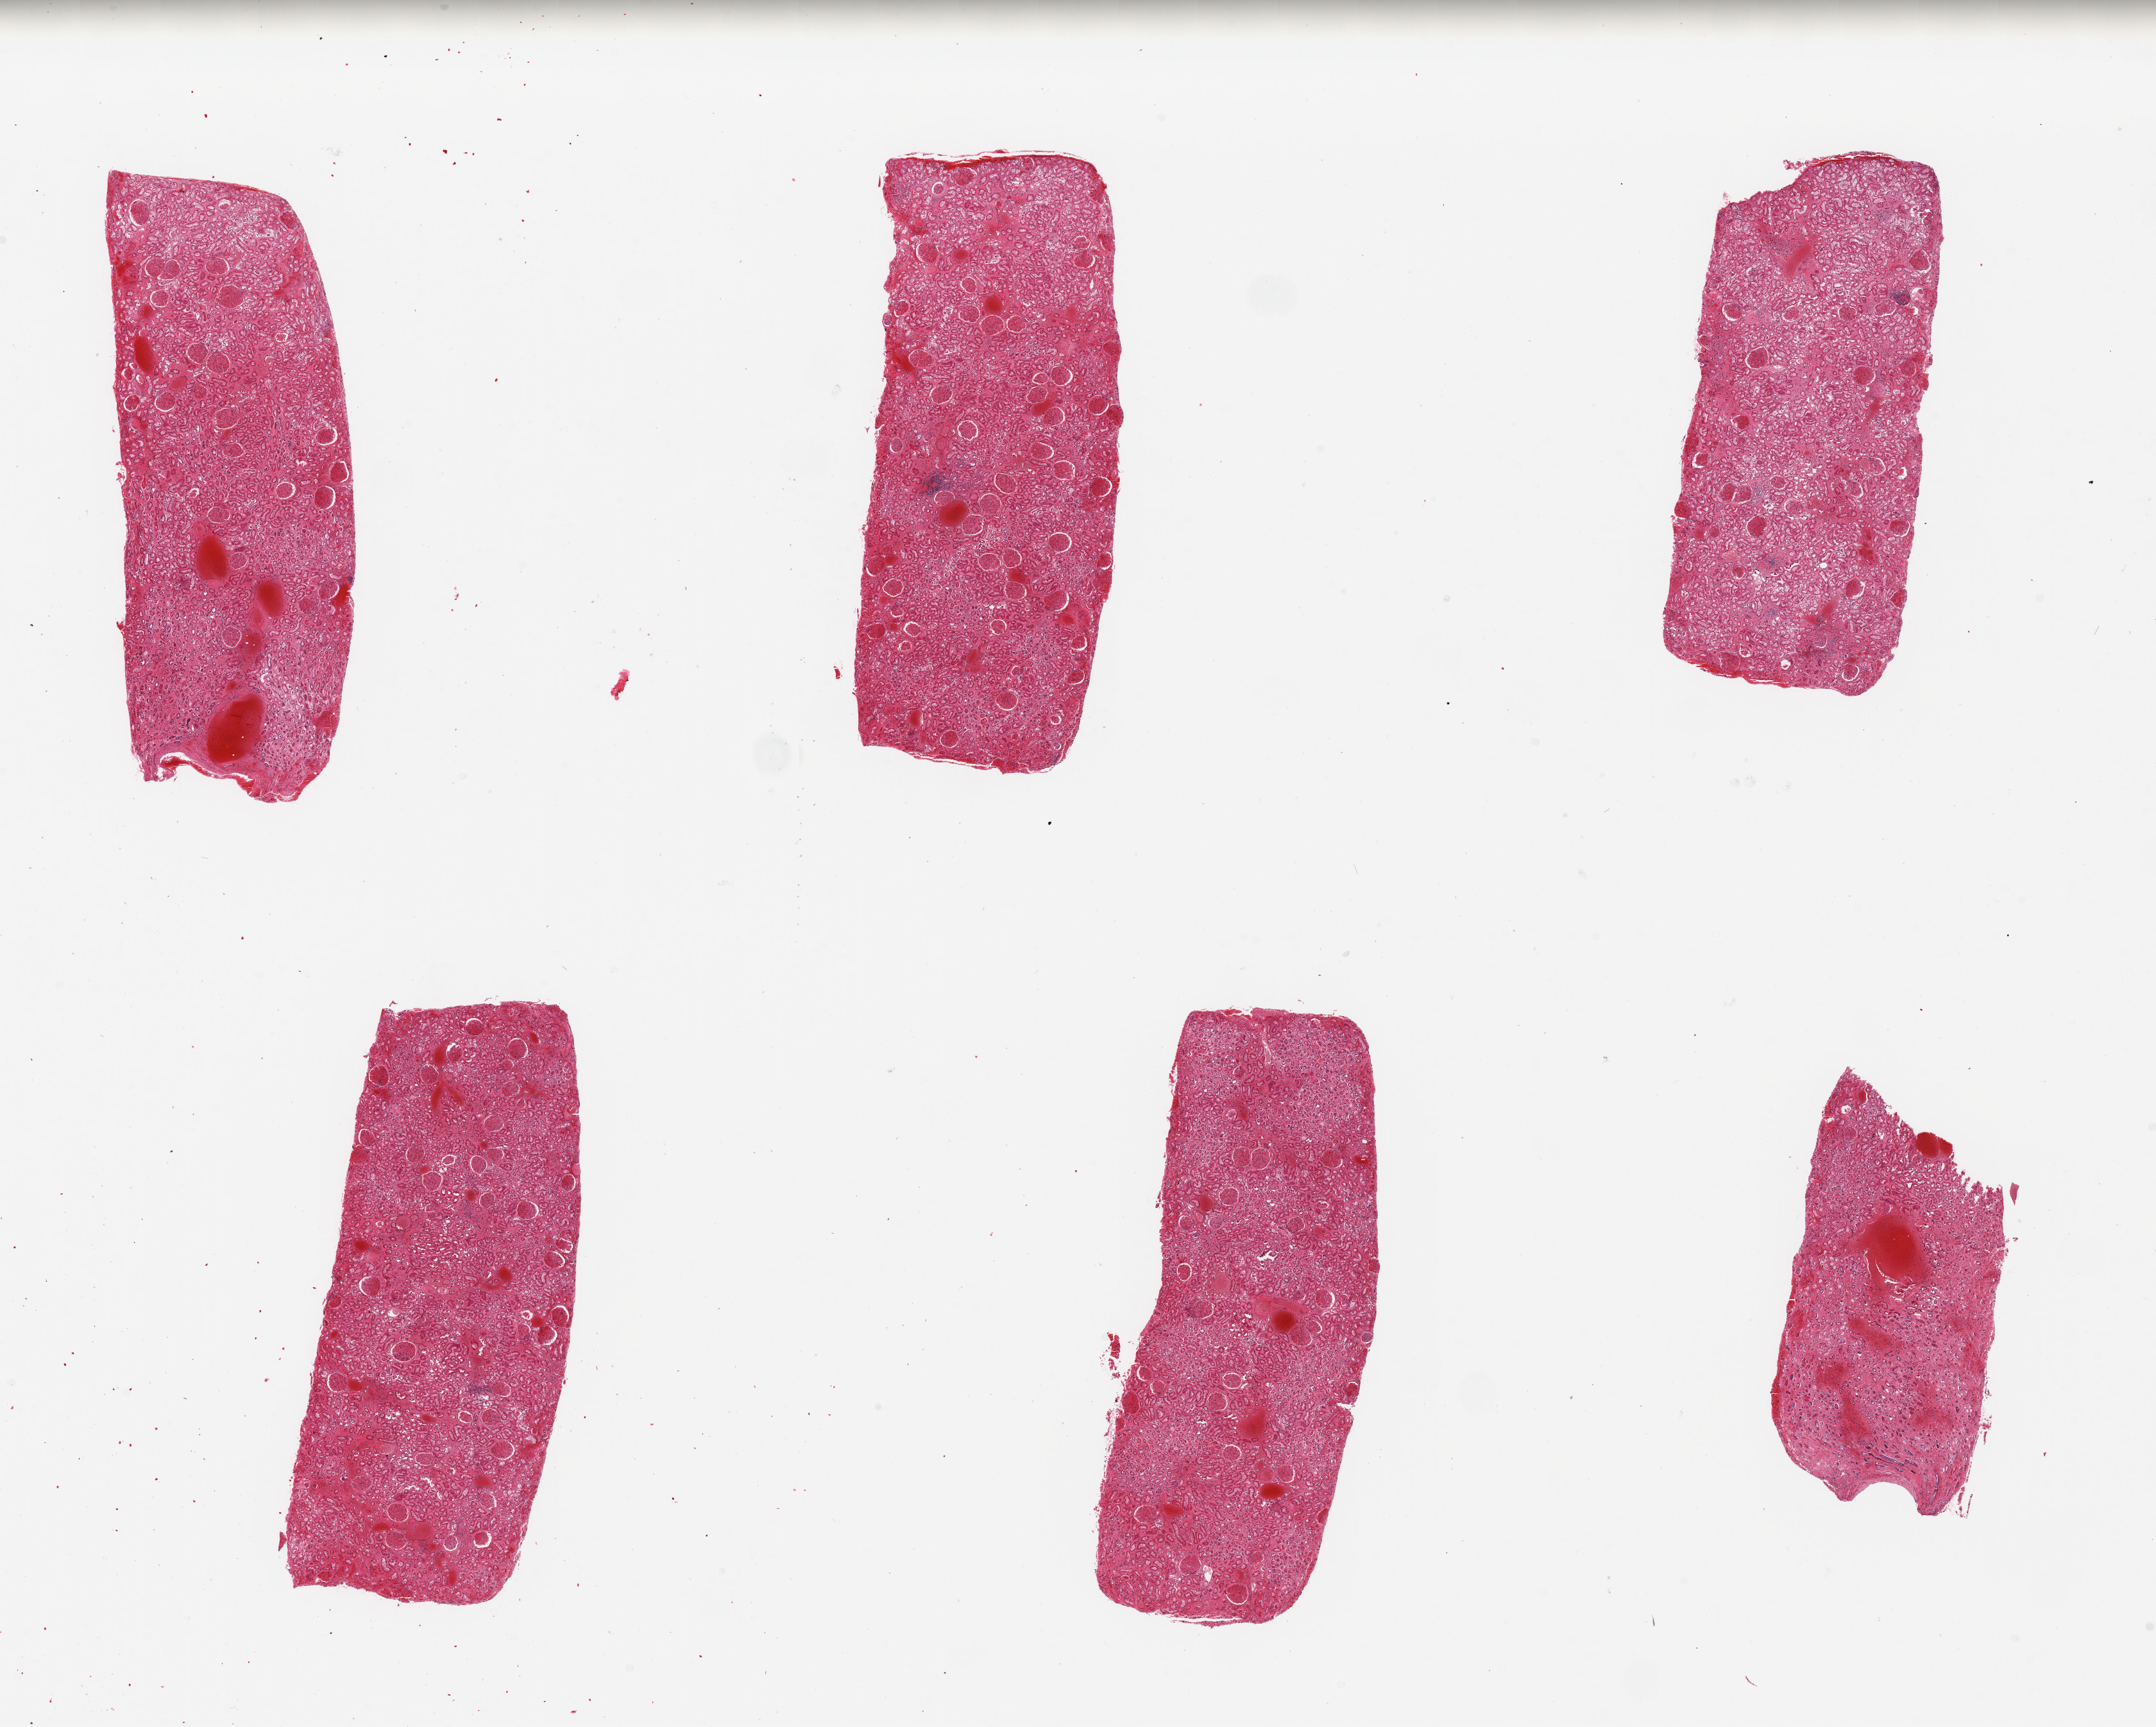
Digitized haematoxylin and eosin-stained section, brightfield, low-resolution overview of the scanned area, about 26.6 x 21.3 mm, PAXgene-fixed, paraffin-embedded tissue, section of renal cortex (target tissue), tissue donor sample.
Pathologist's review note for this sample: 6 pieces ~7x3mm pieces. Congestion, poorly preserved tubules.